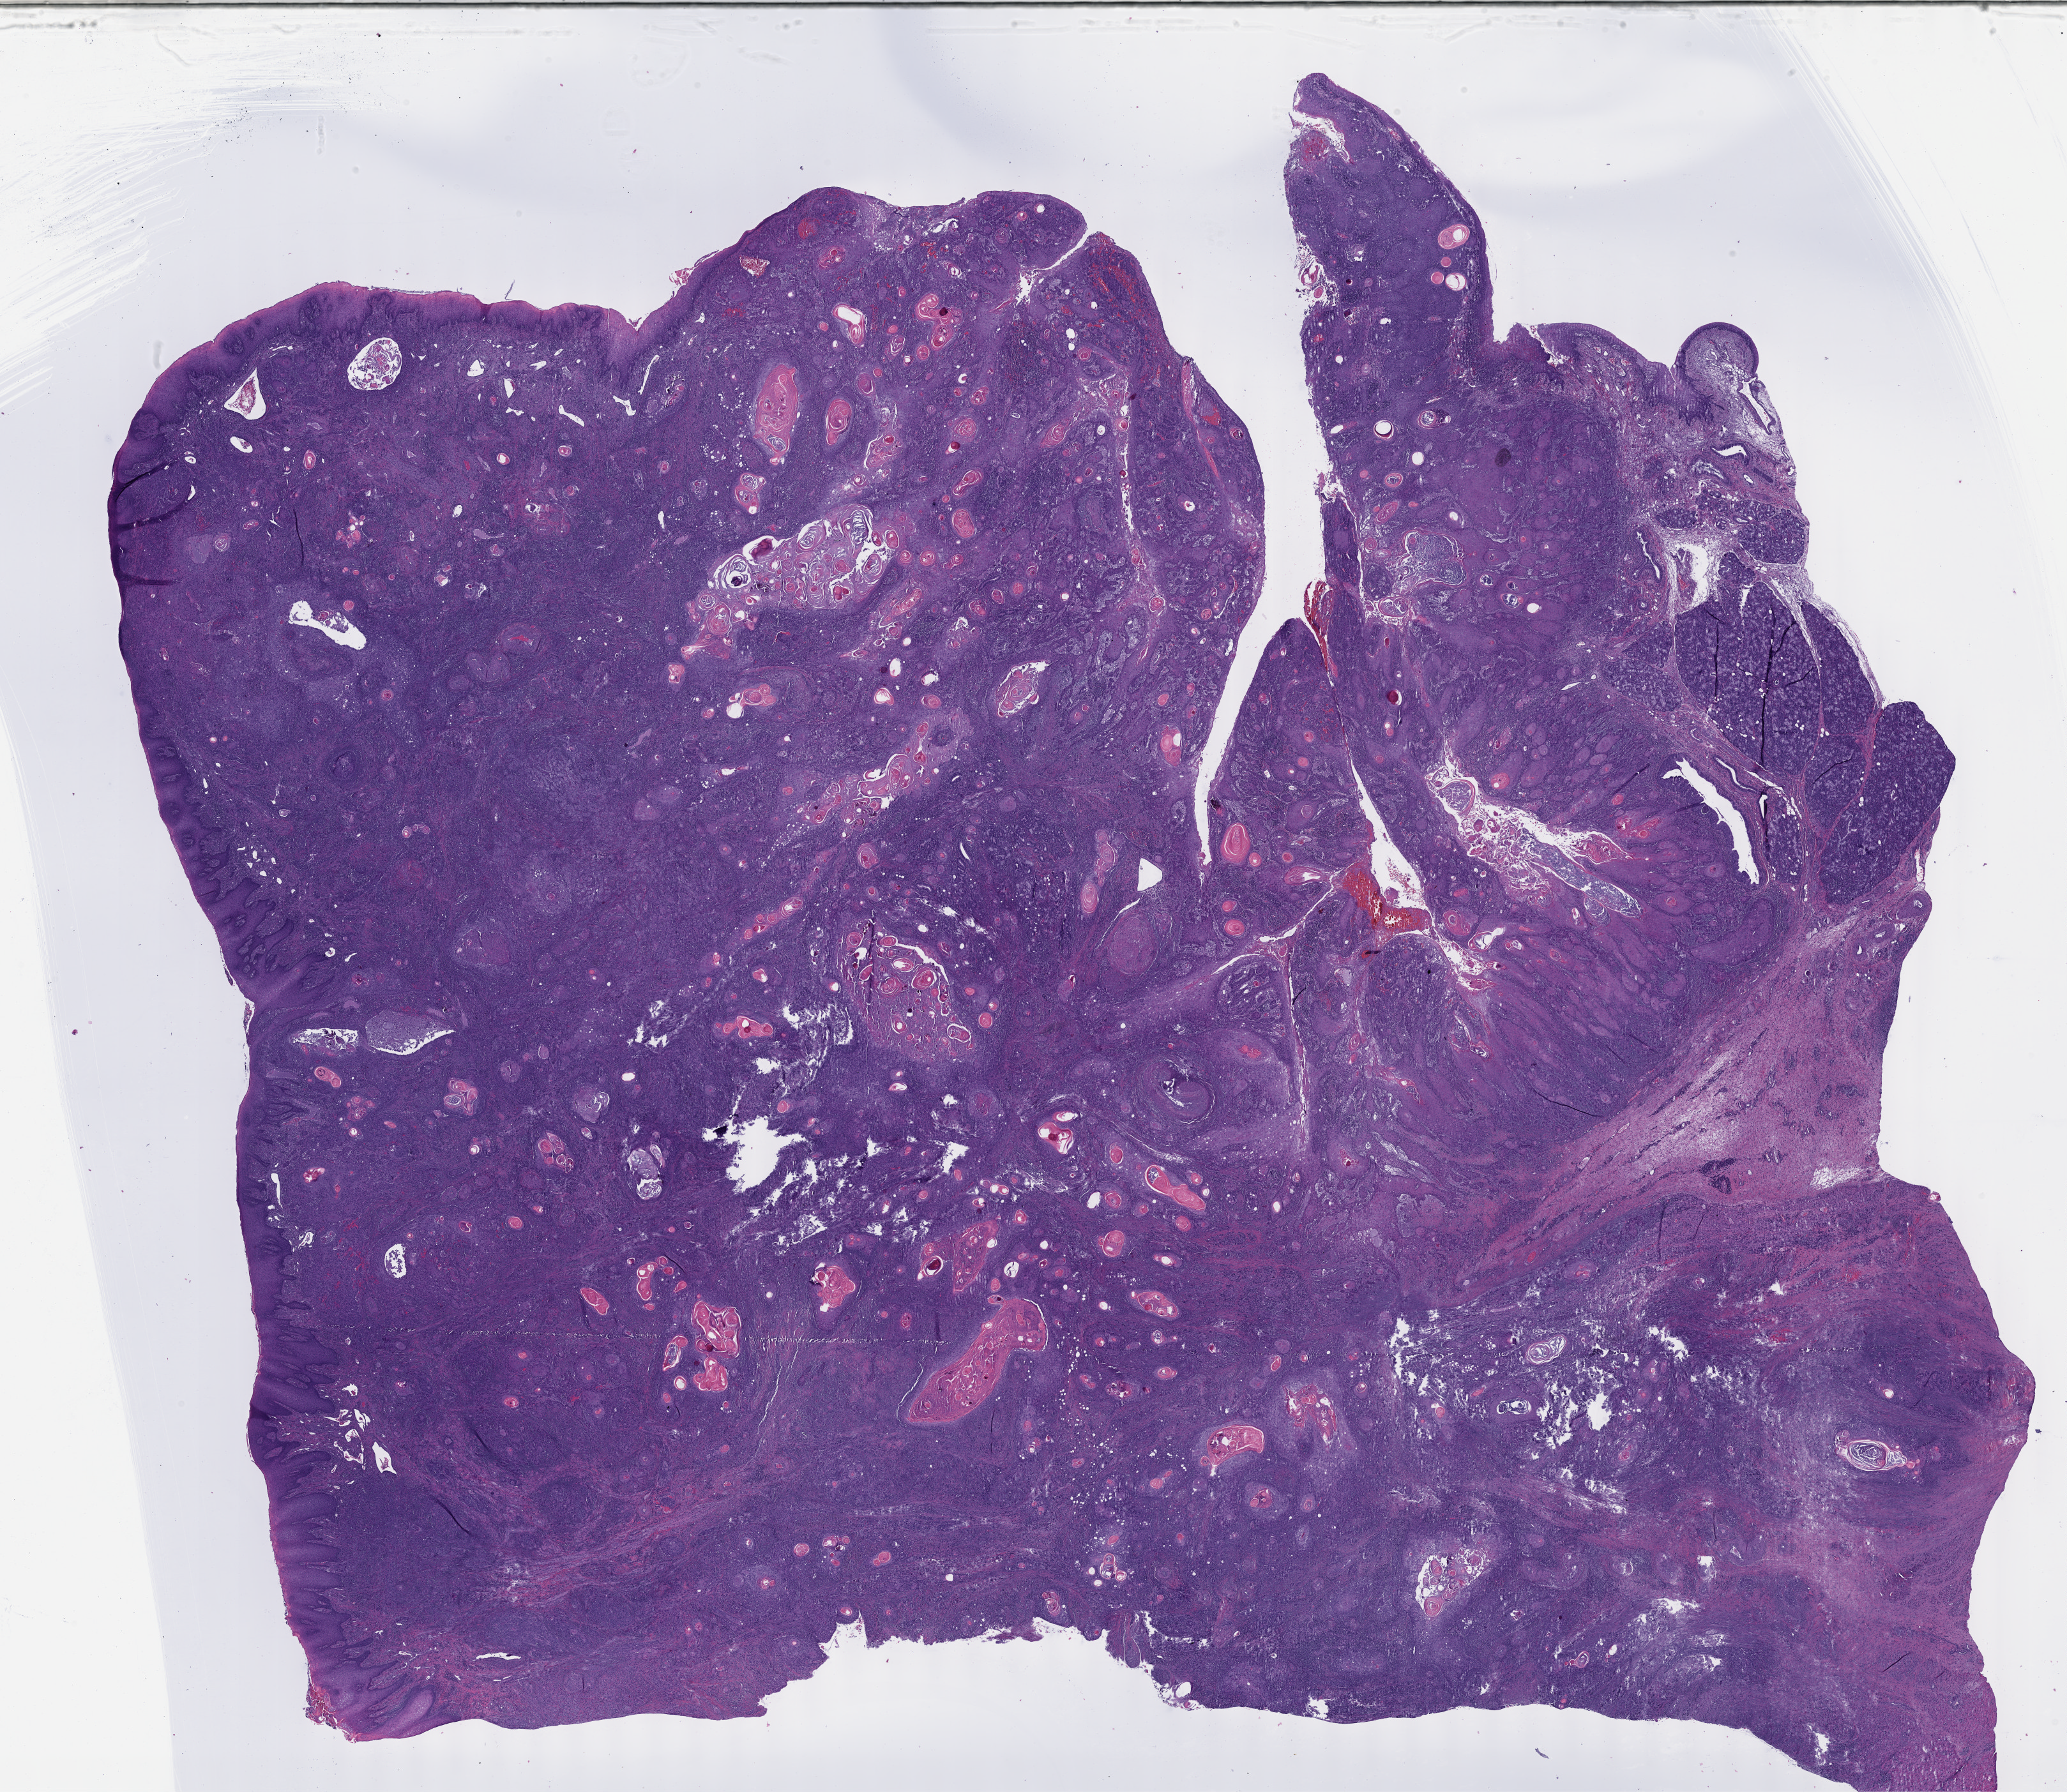
H&E-stained whole-slide image — low-resolution overview of the scanned area, about 26.2 x 22.7 mm, FFPE section, head and neck, primary tumour sample. Patient: male, age at initial diagnosis 59 years. Histologic grade: G2 (moderately differentiated).
• diagnosis: Squamous cell carcinoma, NOS (tongue, NOS)
• AJCC pathologic stage: IVA (7th edition)